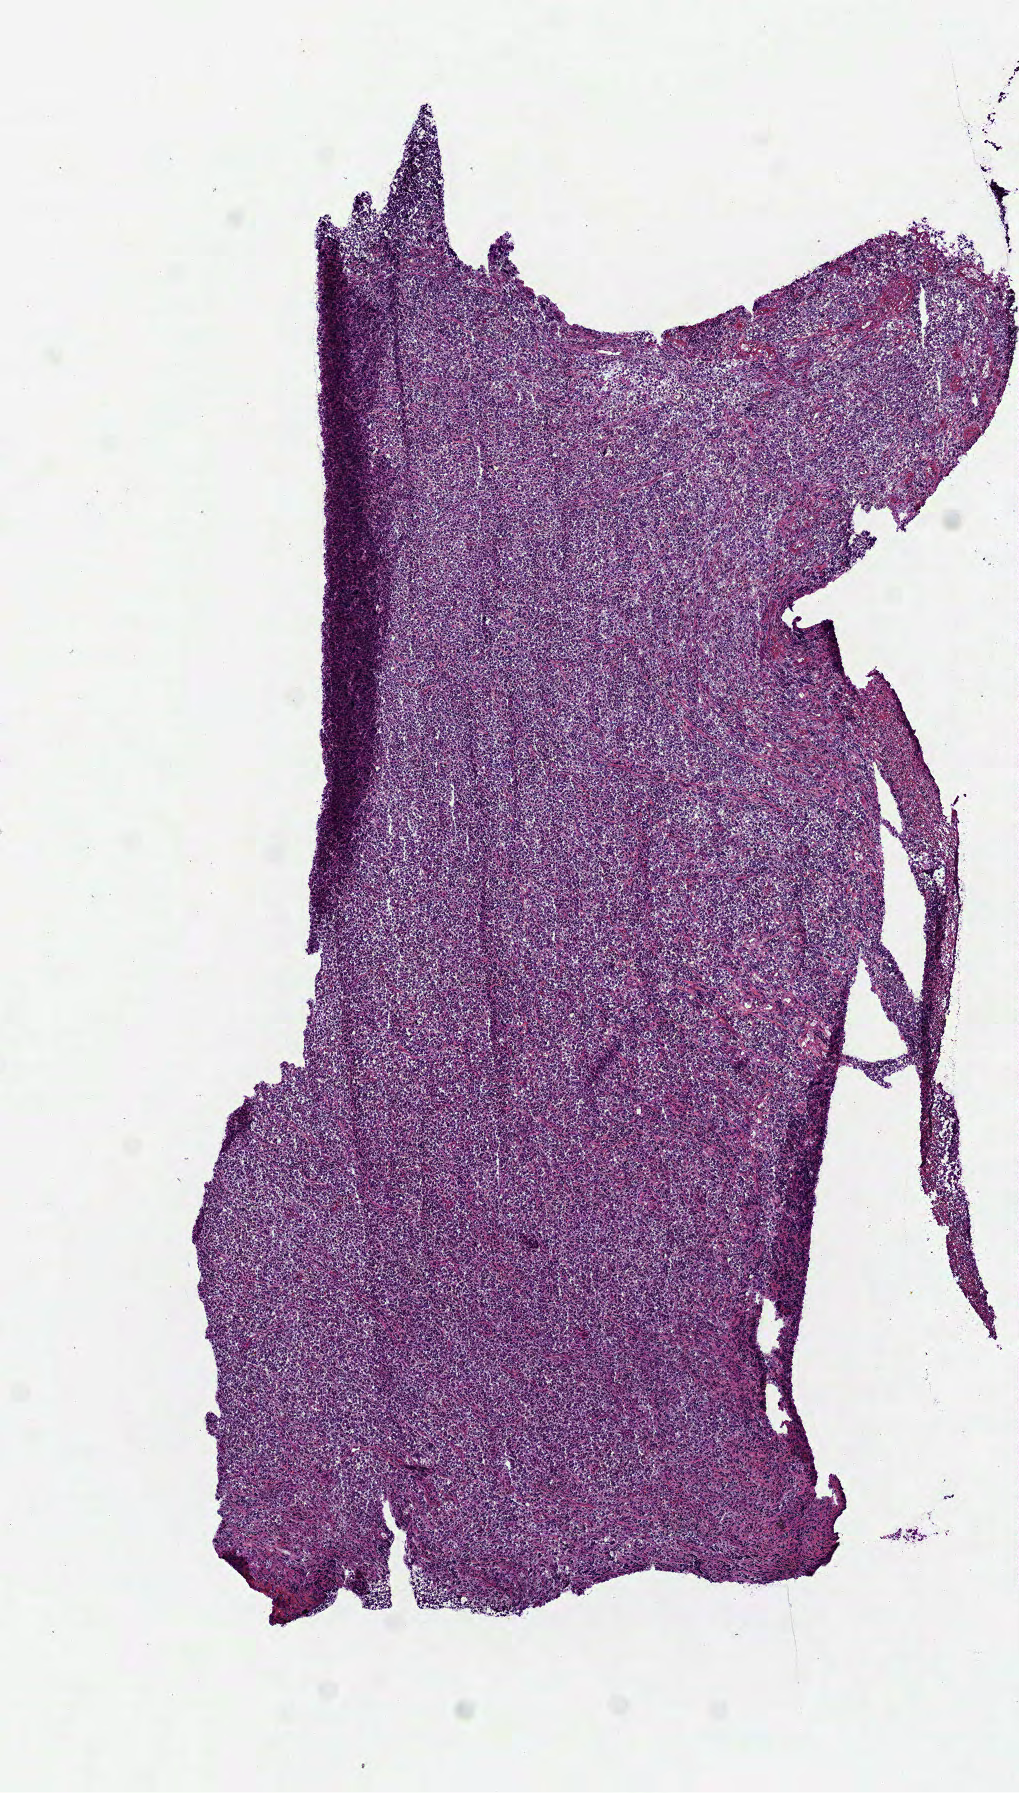
Hematoxylin and eosin (H&E) stained whole-slide image — a low-resolution overview of the entire scanned area, about 4.1 x 7.2 mm; frozen section from the bottom of the tissue portion; lymphoid tissue, primary tumour sample. Female patient; age at initial diagnosis 70 years. Slide review estimates, as recorded: tumour cells 100%, tumour nuclei 91%, normal cells 0%, stromal cells 0%, necrosis 0%. Inflammatory infiltration, as recorded: lymphocyte infiltration 8%, monocyte infiltration 0%, neutrophil infiltration 0%.
Pathologic diagnosis: Diffuse large B-cell lymphoma, NOS (colon, NOS).